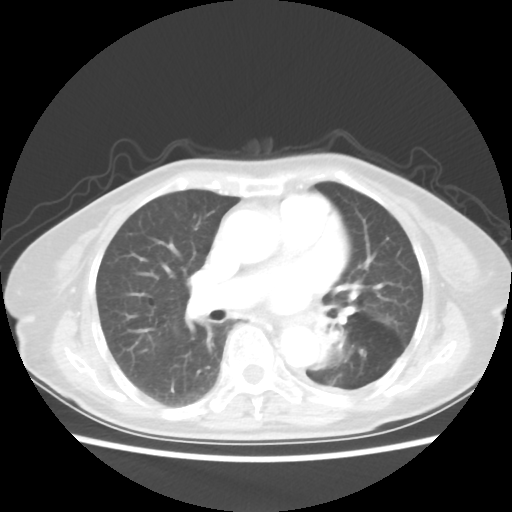
Chest CT, one axial slice; slice 26 of 50 in the series (ordered by position); reconstruction kernel STANDARD; lung window (W 1500 / L -600 HU); 5 mm slice thickness; 512 × 512 image matrix, field of view 335 × 335 mm. Patient: female, 81 years. From the clinical record (not read from this slice): clinical TNM (as recorded): T2 N0 M1a.
Outlined on this slice (rectangle marked by the reading radiologist):
- lung tumour (recorded histology: squamous cell carcinoma): bounding box (x1, y1, x2, y2) in pixels: (312, 328, 348, 371)